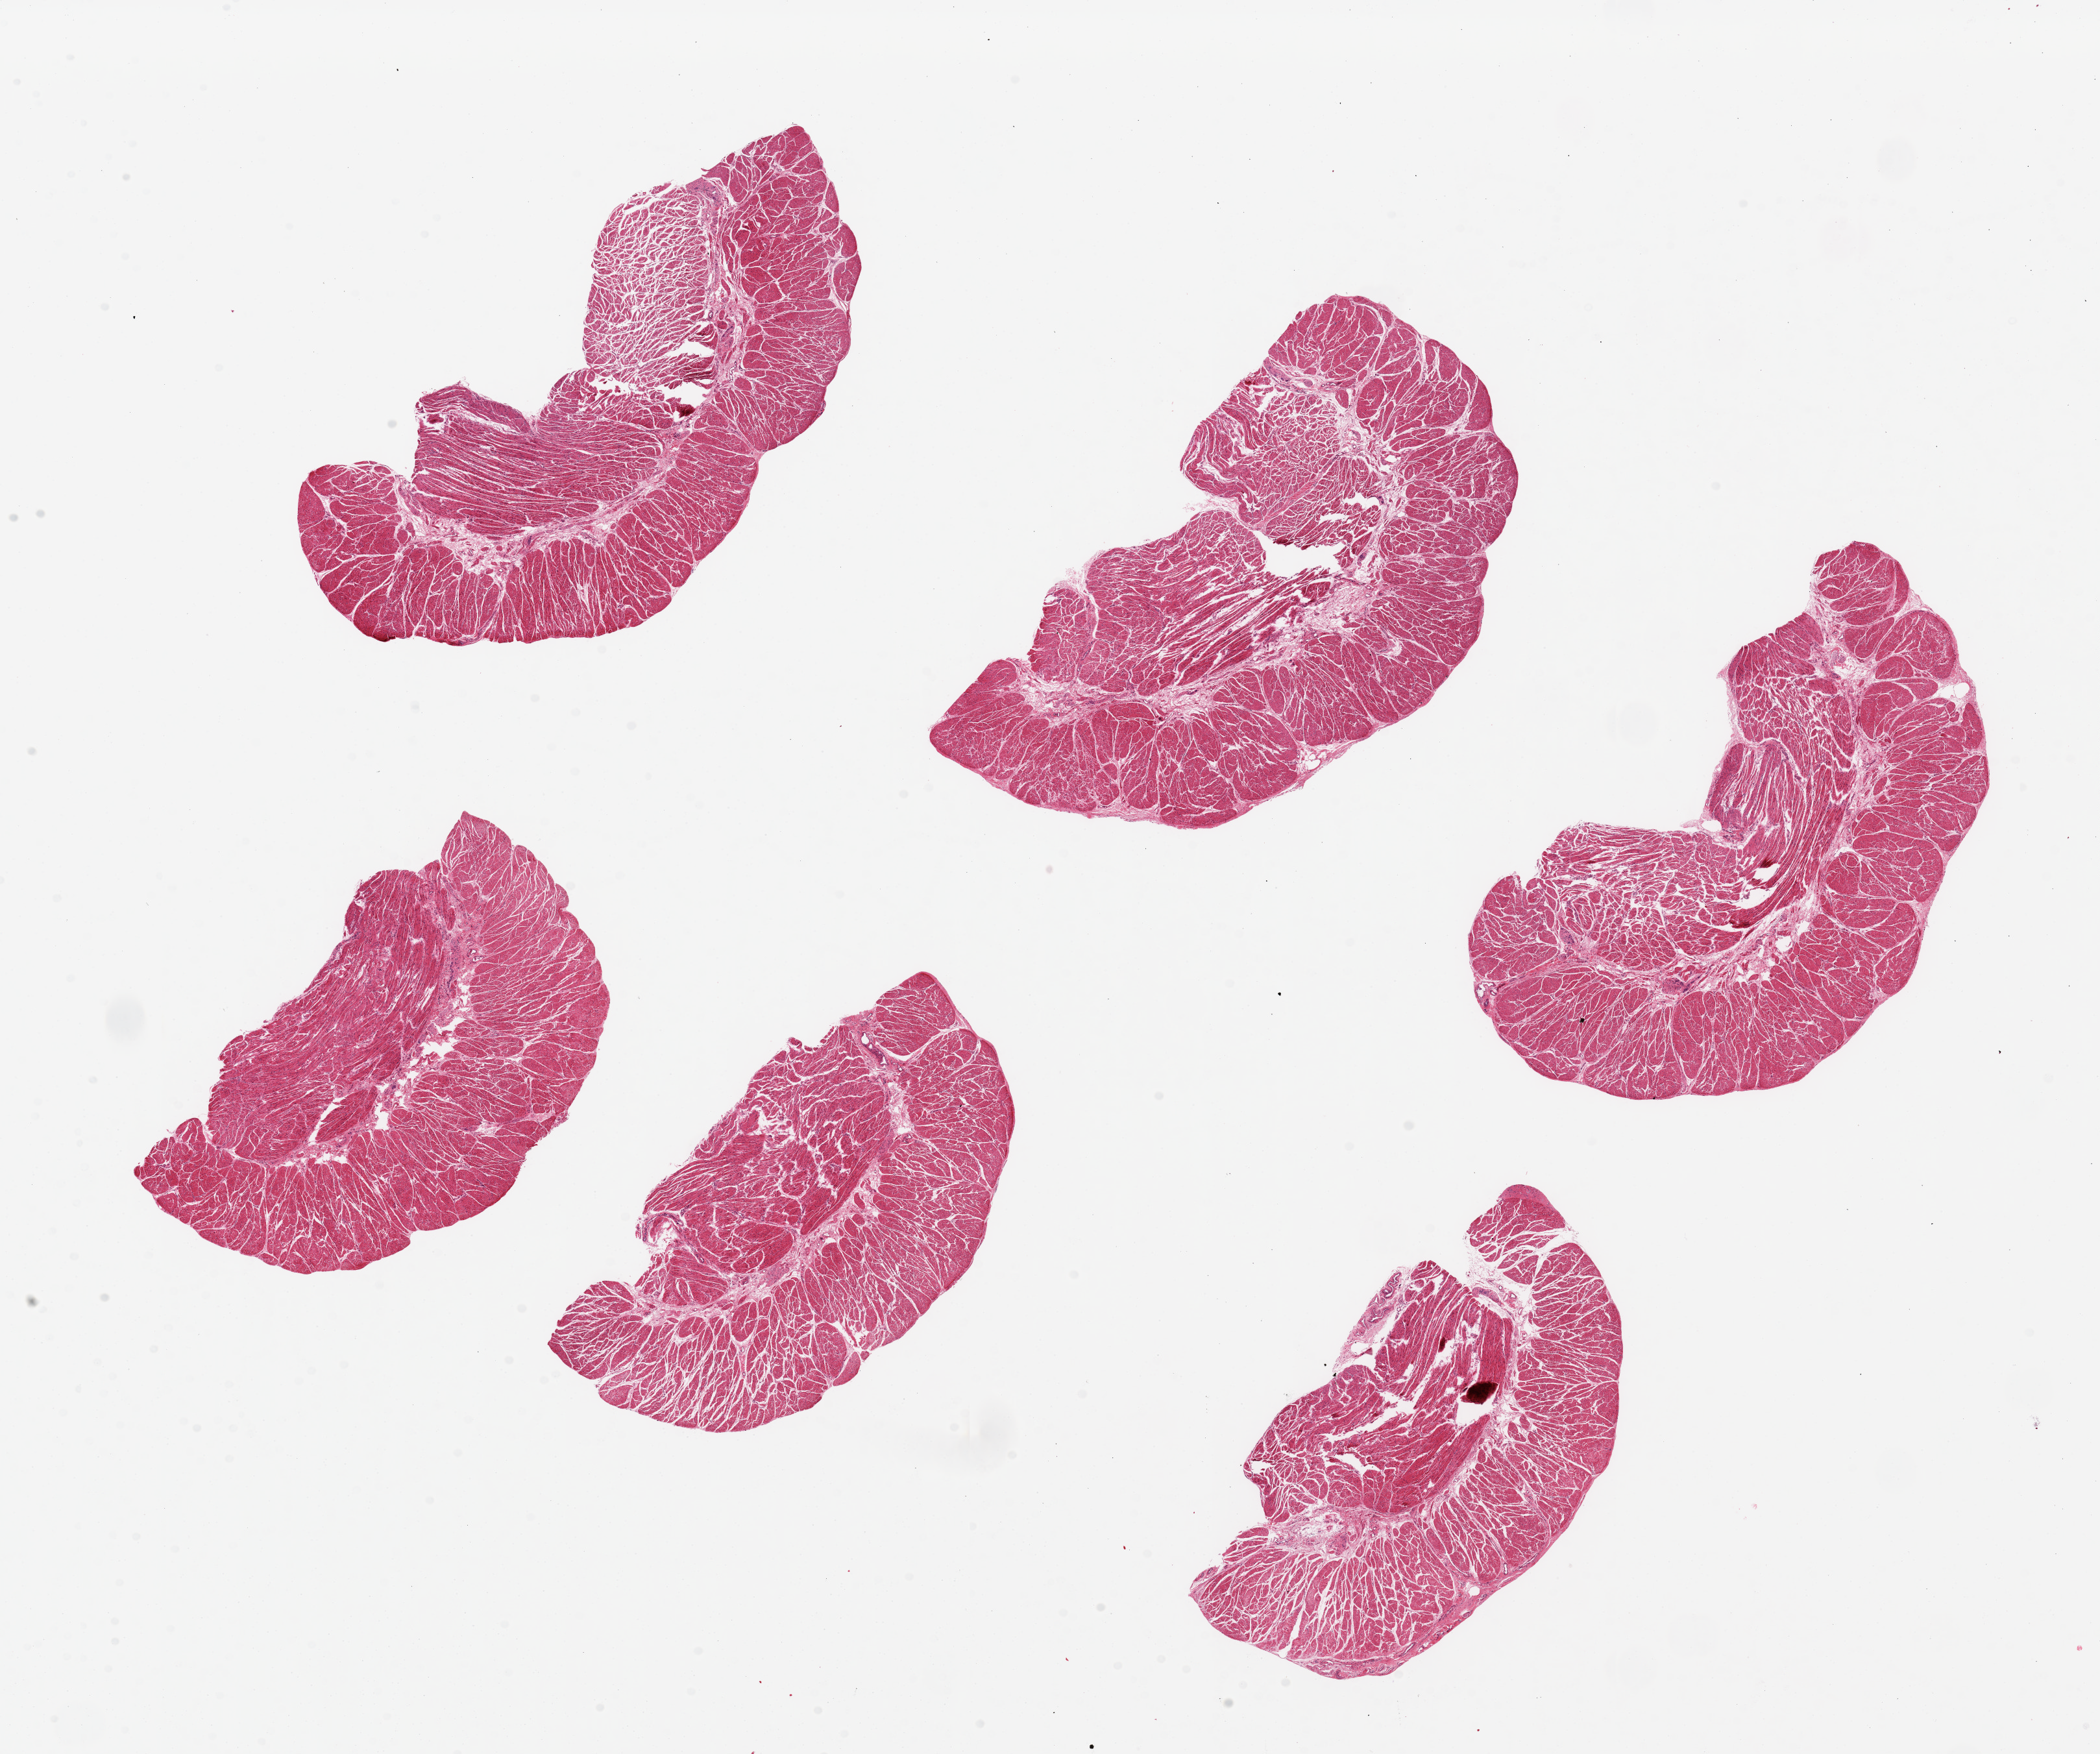
Digitized hematoxylin and eosin (H&E)-stained section, whole scanned area (about 25.6 x 21.4 mm) shown as a low-resolution overview, PAXgene-fixed paraffin-embedded (PFPE) section, sampled site (target tissue): esophageal muscle, tissue donor sample. Donor: female.
Review note (as recorded): 6 pieces, up to 8x5mm; well sampled.